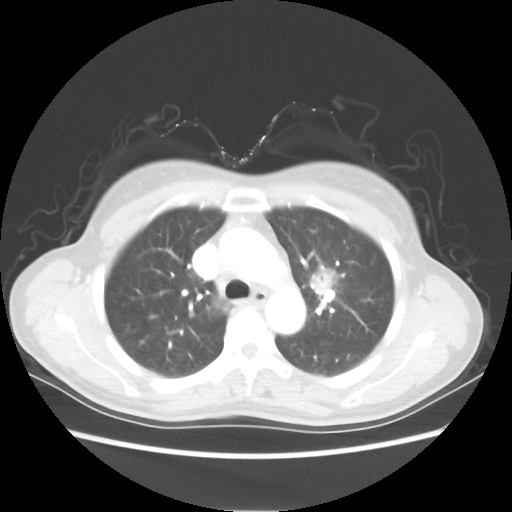
Chest CT, one axial slice. Slice 38 of 54 in the series (ordered by position). Lung window (W 1500 / L -600 HU). 512 × 512 image matrix. Female patient, age 53 years. Case-level facts recorded for this patient, not image findings: clinical TNM (as recorded): T1c N0 M0.
Structures marked on this image (bounding box drawn by a radiologist):
- lung tumour (recorded histology: adenocarcinoma): bounding box (x1, y1, x2, y2) in pixels: (307, 262, 336, 299)
- lung tumour (recorded histology: adenocarcinoma): (308, 263, 338, 304)